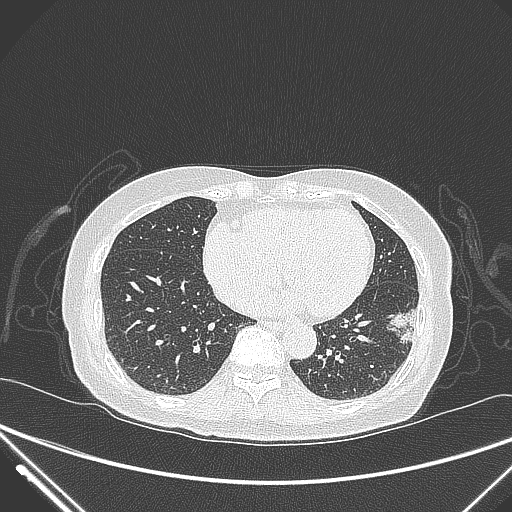
Chest CT, one axial slice; lung window (W 1500 / L -600 HU); 512 × 512 image matrix, field of view 377 × 377 mm. Patient: female, 82 years. Case-level facts recorded for this patient, not image findings: clinical TNM (as recorded): T1c N0 M0; histopathological grade: G2.
Structures marked on this image (bounding box drawn by a radiologist):
- lung tumour (recorded histology: adenocarcinoma): bounding box <384,303,421,344> (left, top, right, bottom; pixels)